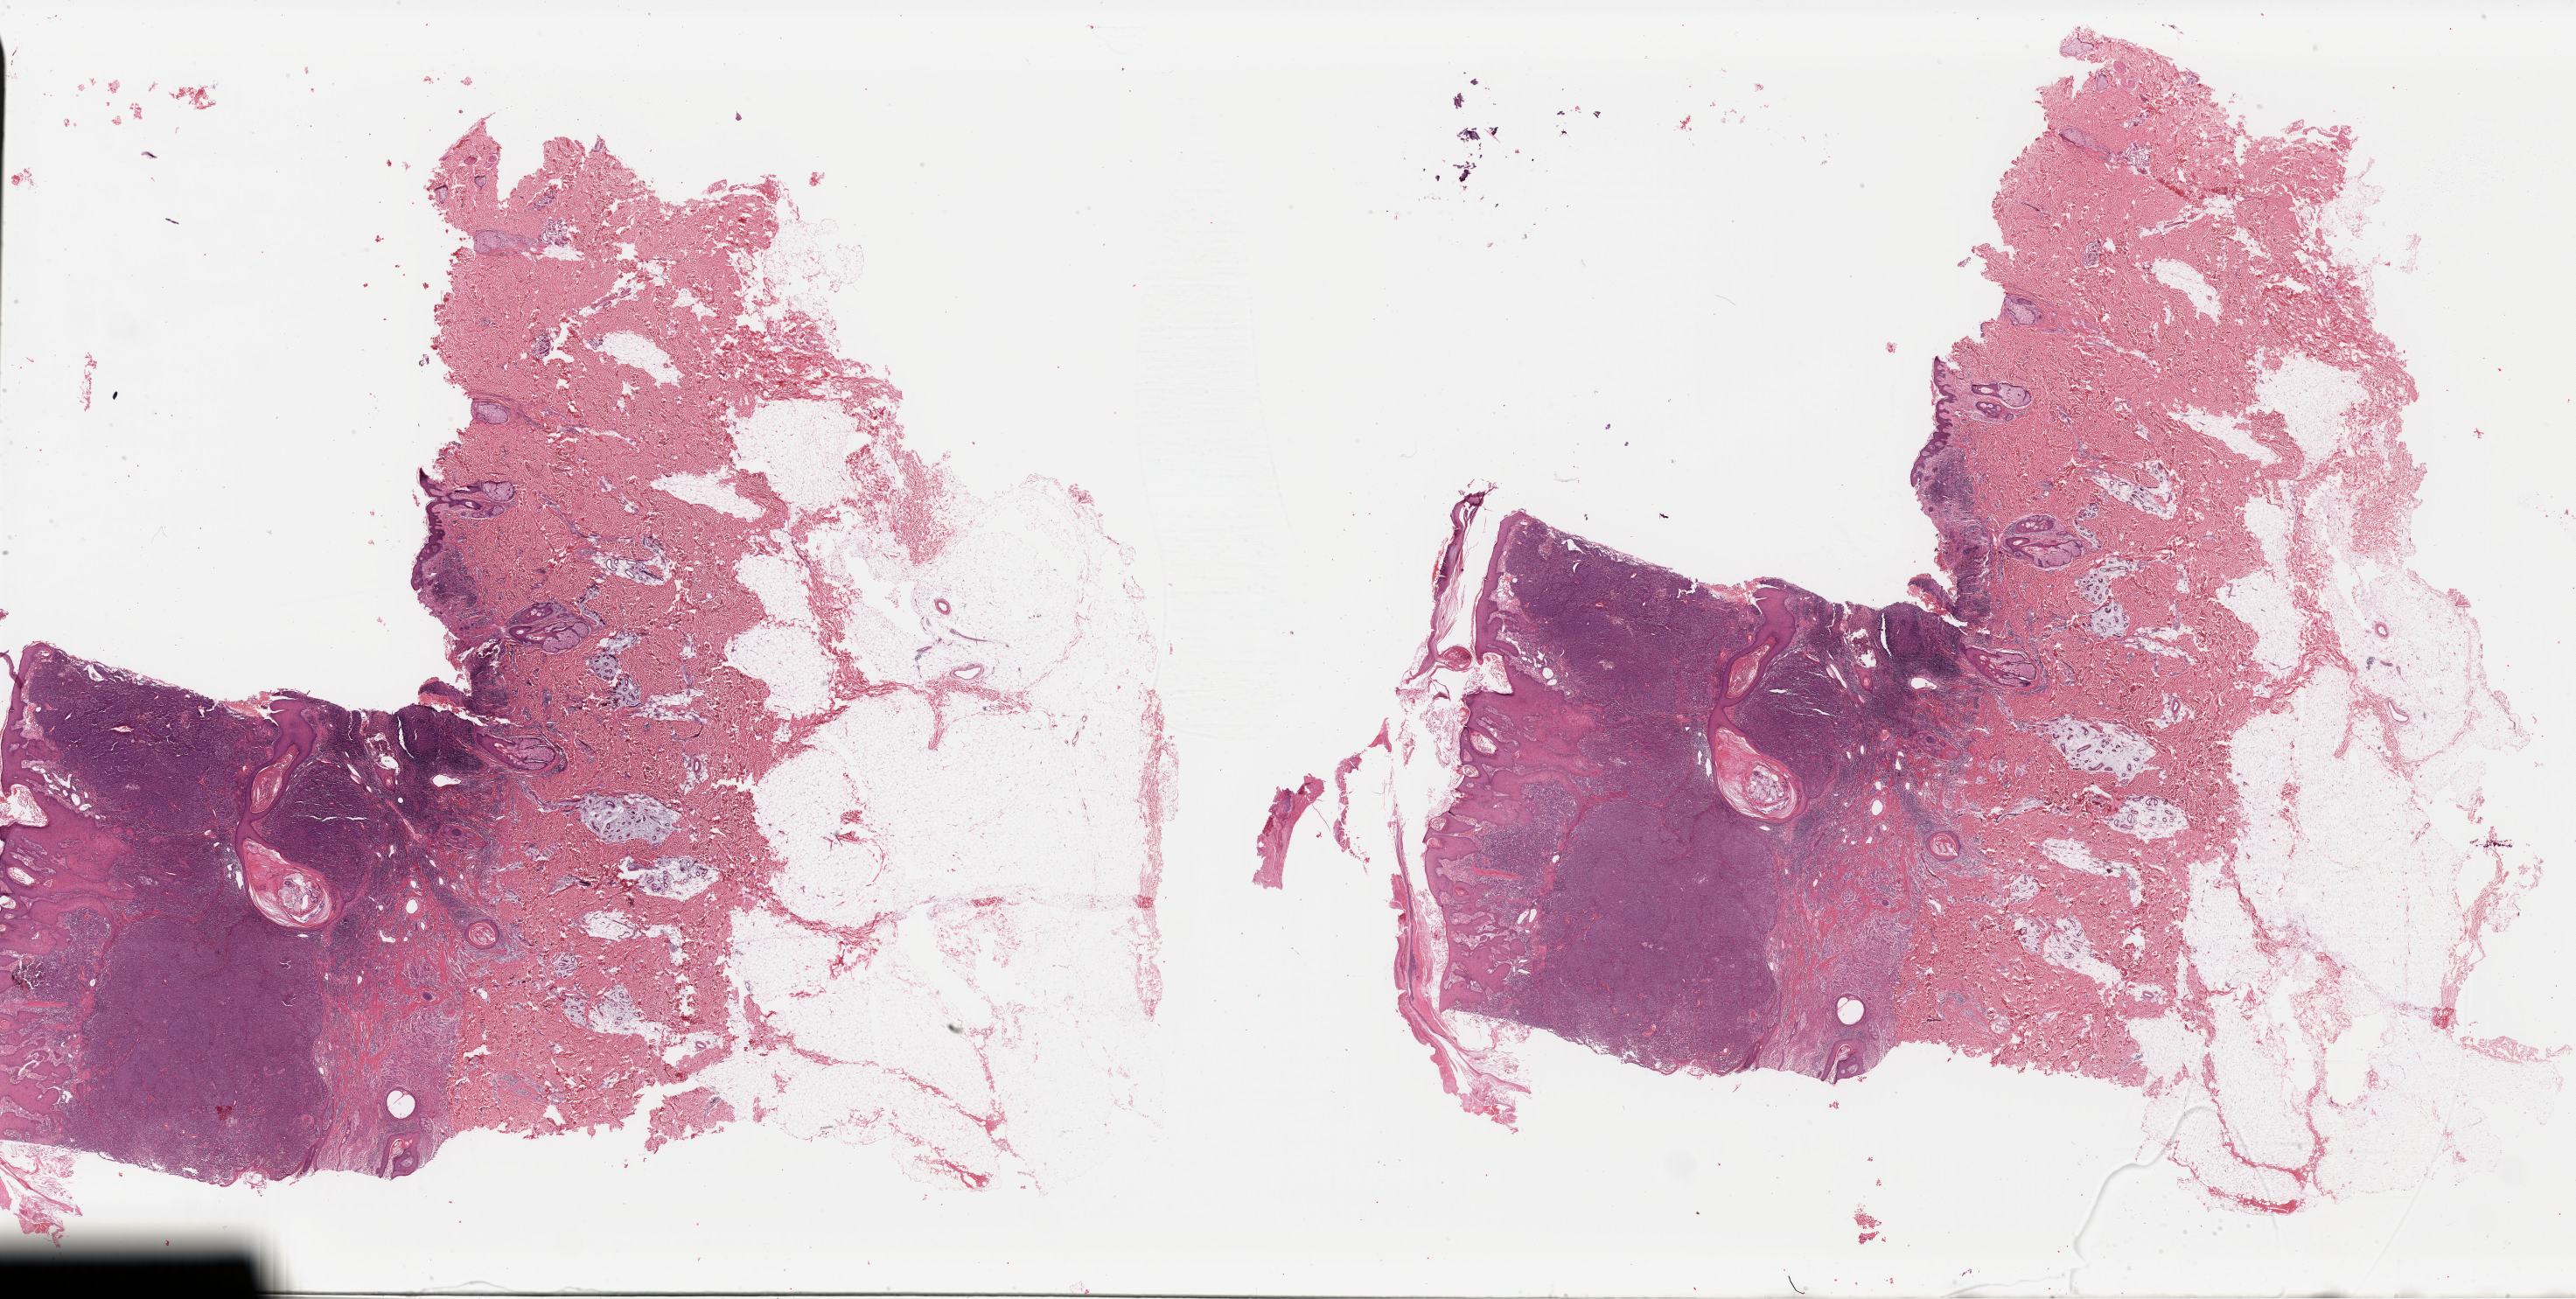
Whole-slide histology image, H&E, whole scanned area (about 46.3 x 23.3 mm) shown as a low-resolution overview, FFPE section, skin, primary tumour sample. Male, age 43 years at initial diagnosis.
Pathologic diagnosis: Malignant melanoma, NOS. AJCC pathologic stage: IIIA (5th edition).